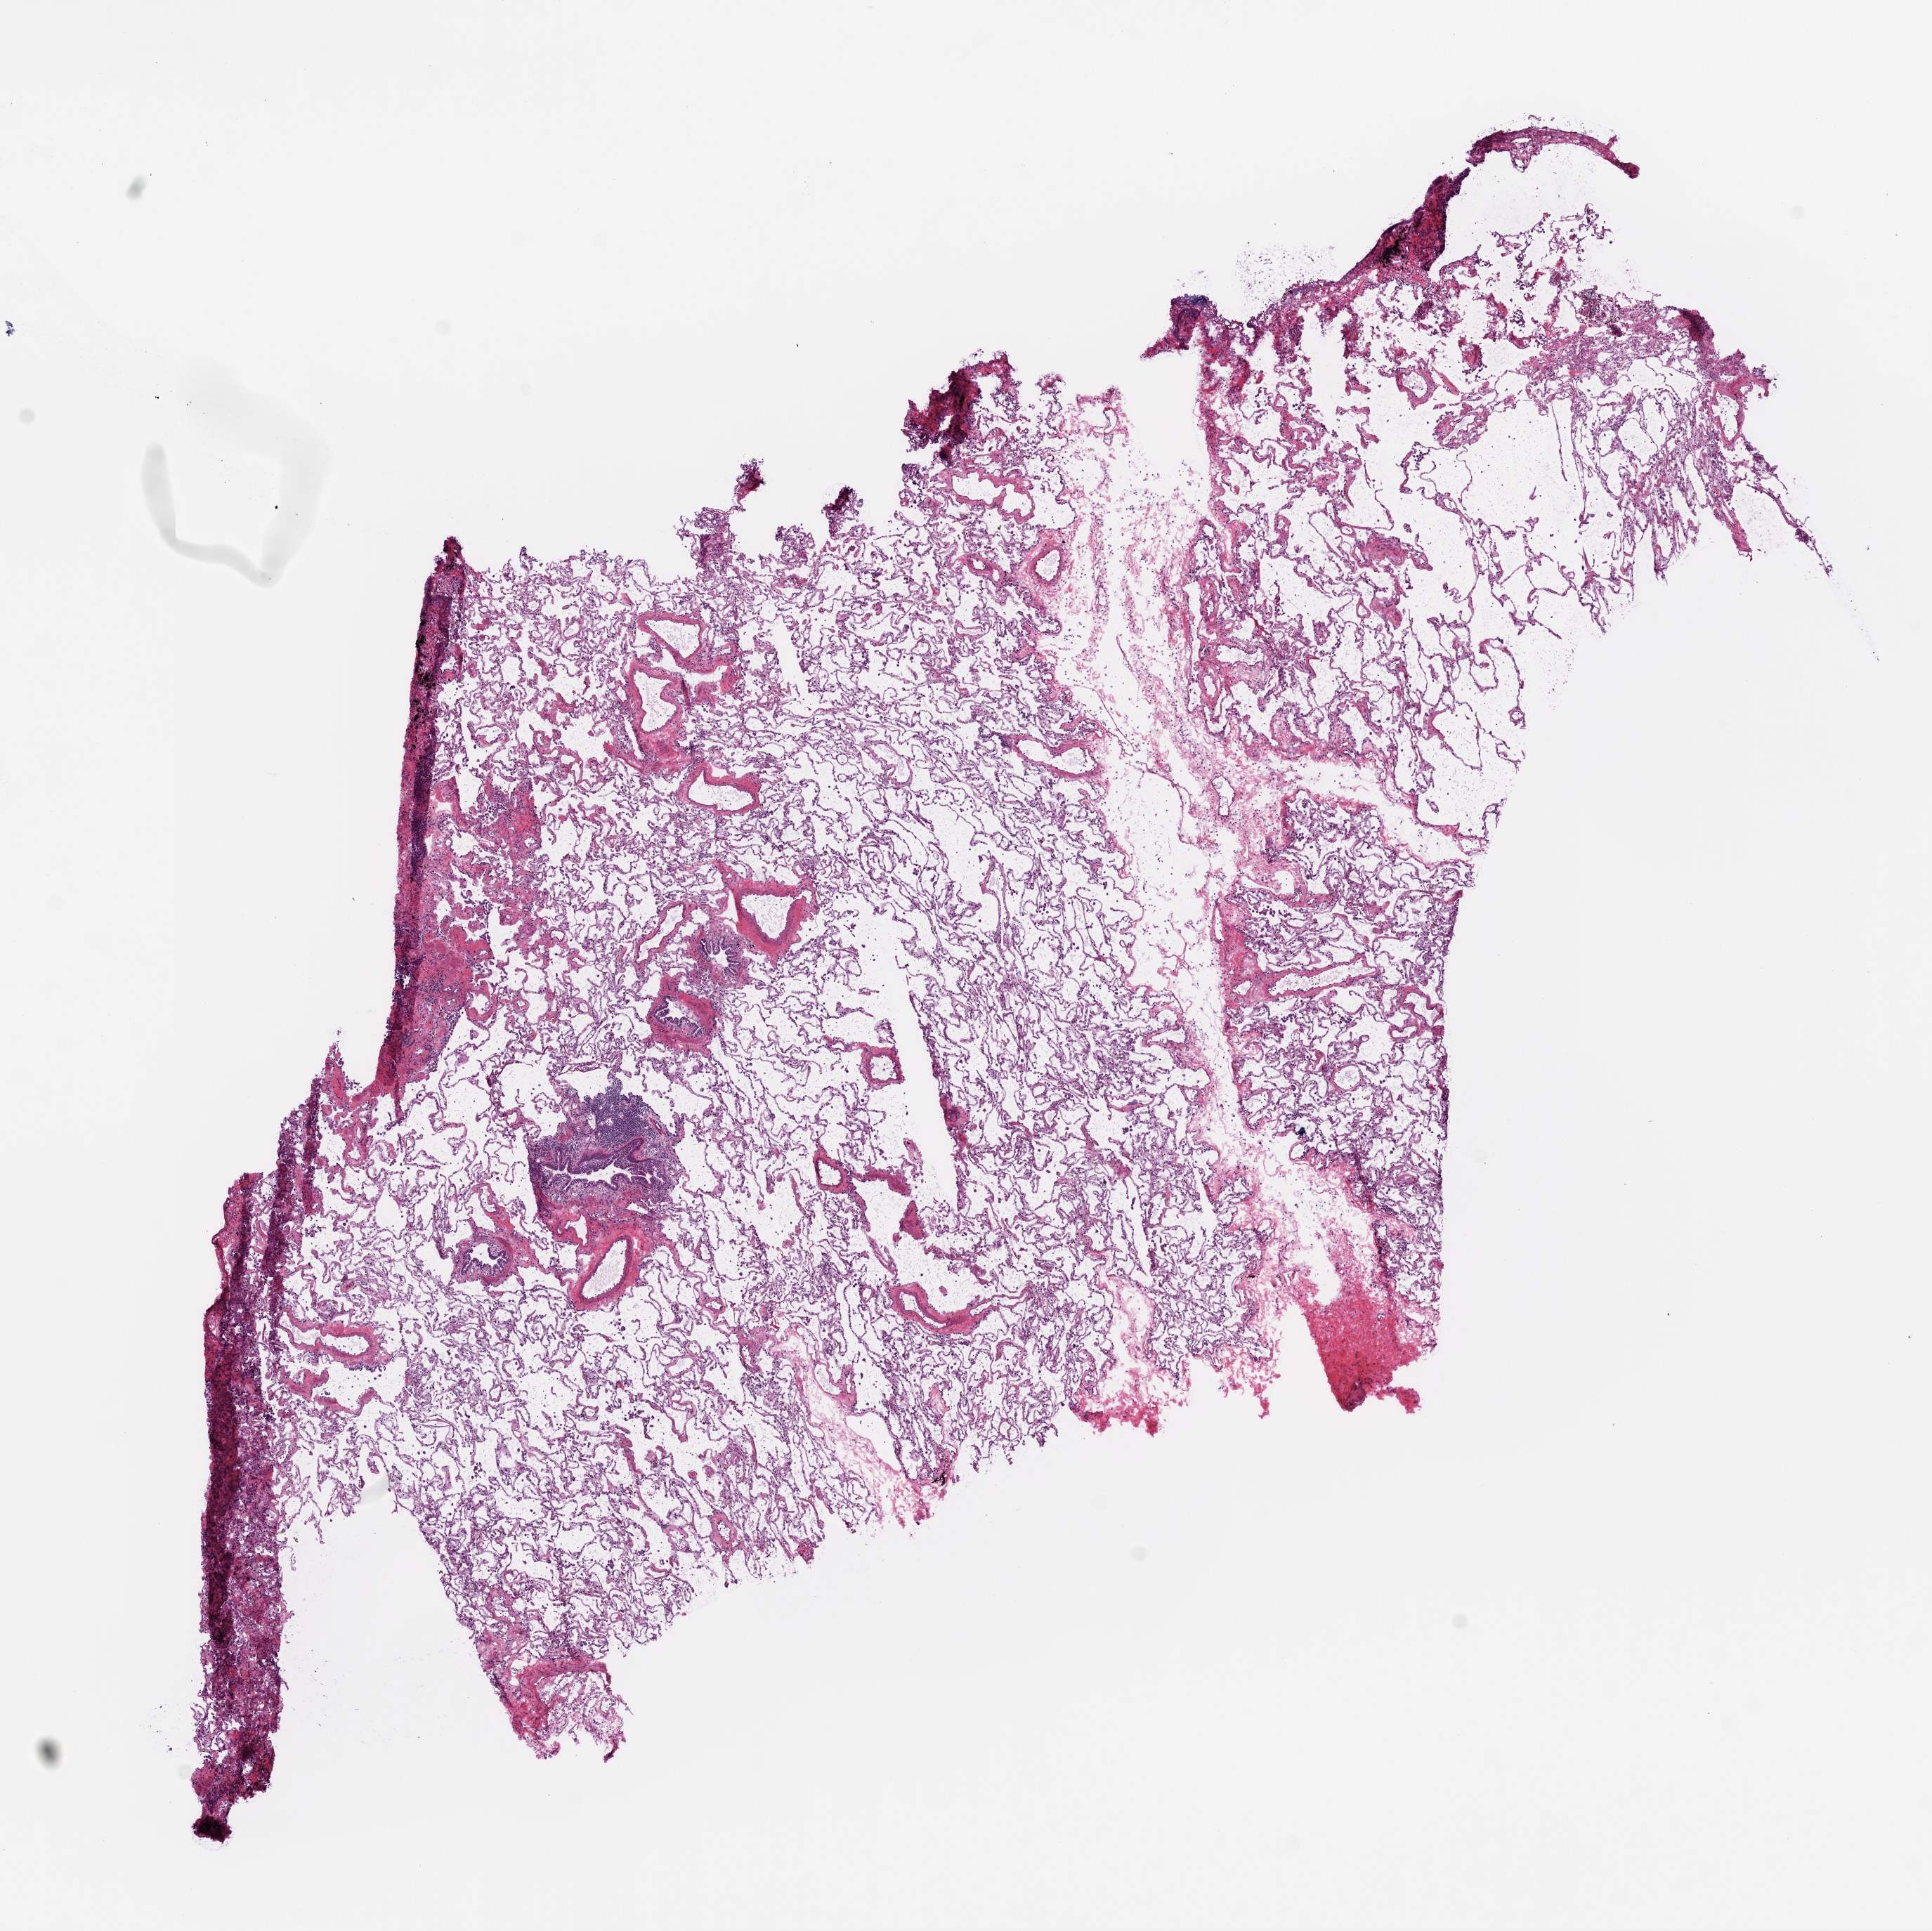
Digitized H&E tissue section (whole slide) — shown as a low-resolution overview of the whole scanned area (about 11.0 x 11.0 mm, from a 20x scan). Frozen section from the bottom of the tissue portion. Sample: solid tissue normal (non-tumour tissue), lung. Male patient; age at initial diagnosis 73 years.
This section: solid tissue normal (non-tumour) sample from the same patient. Patient diagnosis: Squamous cell carcinoma, NOS.